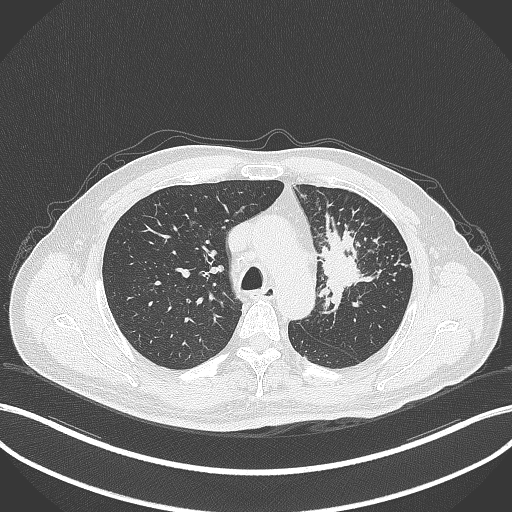
Chest CT, one axial slice. Position 250 of 386 along the scan axis. Reconstruction kernel B70f. Lung window (W 1500 / L -600 HU). 512 × 512 image matrix. Male patient, age 69 years. Case-level facts recorded for this patient, not image findings: clinical TNM (as recorded): T2a N2 M0; histopathological grade: G2-3.
Annotated regions visible in this slice (rectangle marked by the reading radiologist):
- lung tumour (recorded histology: adenocarcinoma): bounding box (x1, y1, x2, y2) in pixels: (314, 222, 370, 309)